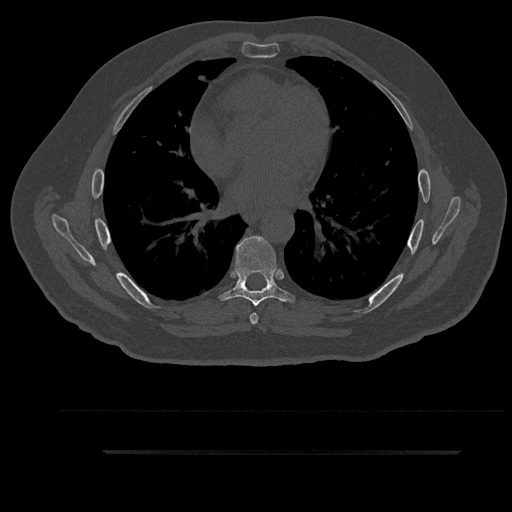
CT including the spine, one axial slice. Slice 535 of 797 in the series (ordered by position). Reconstruction kernel Br40s/3. Bone window (W 1800 / L 400 HU). 512 × 512 image matrix, field of view 432 × 432 mm. Patient: male, 63 years. From the clinical record (not read from this slice): primary cancer: renal; vertebrae with lytic lesions (as recorded): T8.
Outlined on this slice (semi-automatically segmented with operator editing):
- T6 vertebra: bounding box (x1, y1, x2, y2) in pixels: (250, 289, 262, 325)
- T7 vertebra: (219, 236, 295, 306)